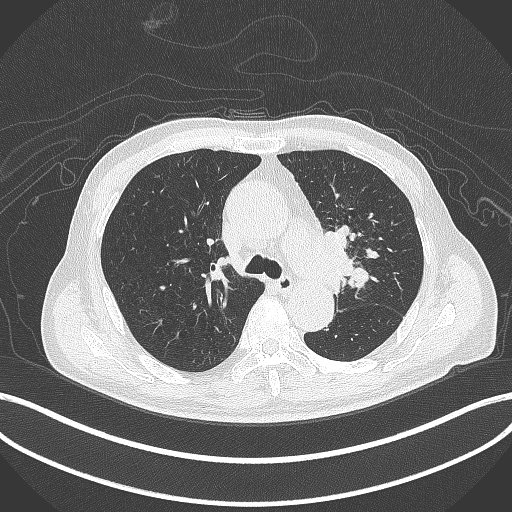
Chest CT, one axial slice. Position 290 of 417 along the scan axis. Lung window (W 1500 / L -600 HU). 1 mm slice thickness. 512 × 512 image matrix, field of view 400 × 400 mm. Male patient, age 77 years. Case-level facts recorded for this patient, not image findings: clinical TNM (as recorded): T3 N1 M0.
Outlined on this slice (bounding box drawn by a radiologist):
- lung tumour (recorded histology: adenocarcinoma): box from (x=312, y=227) to (x=355, y=284) px